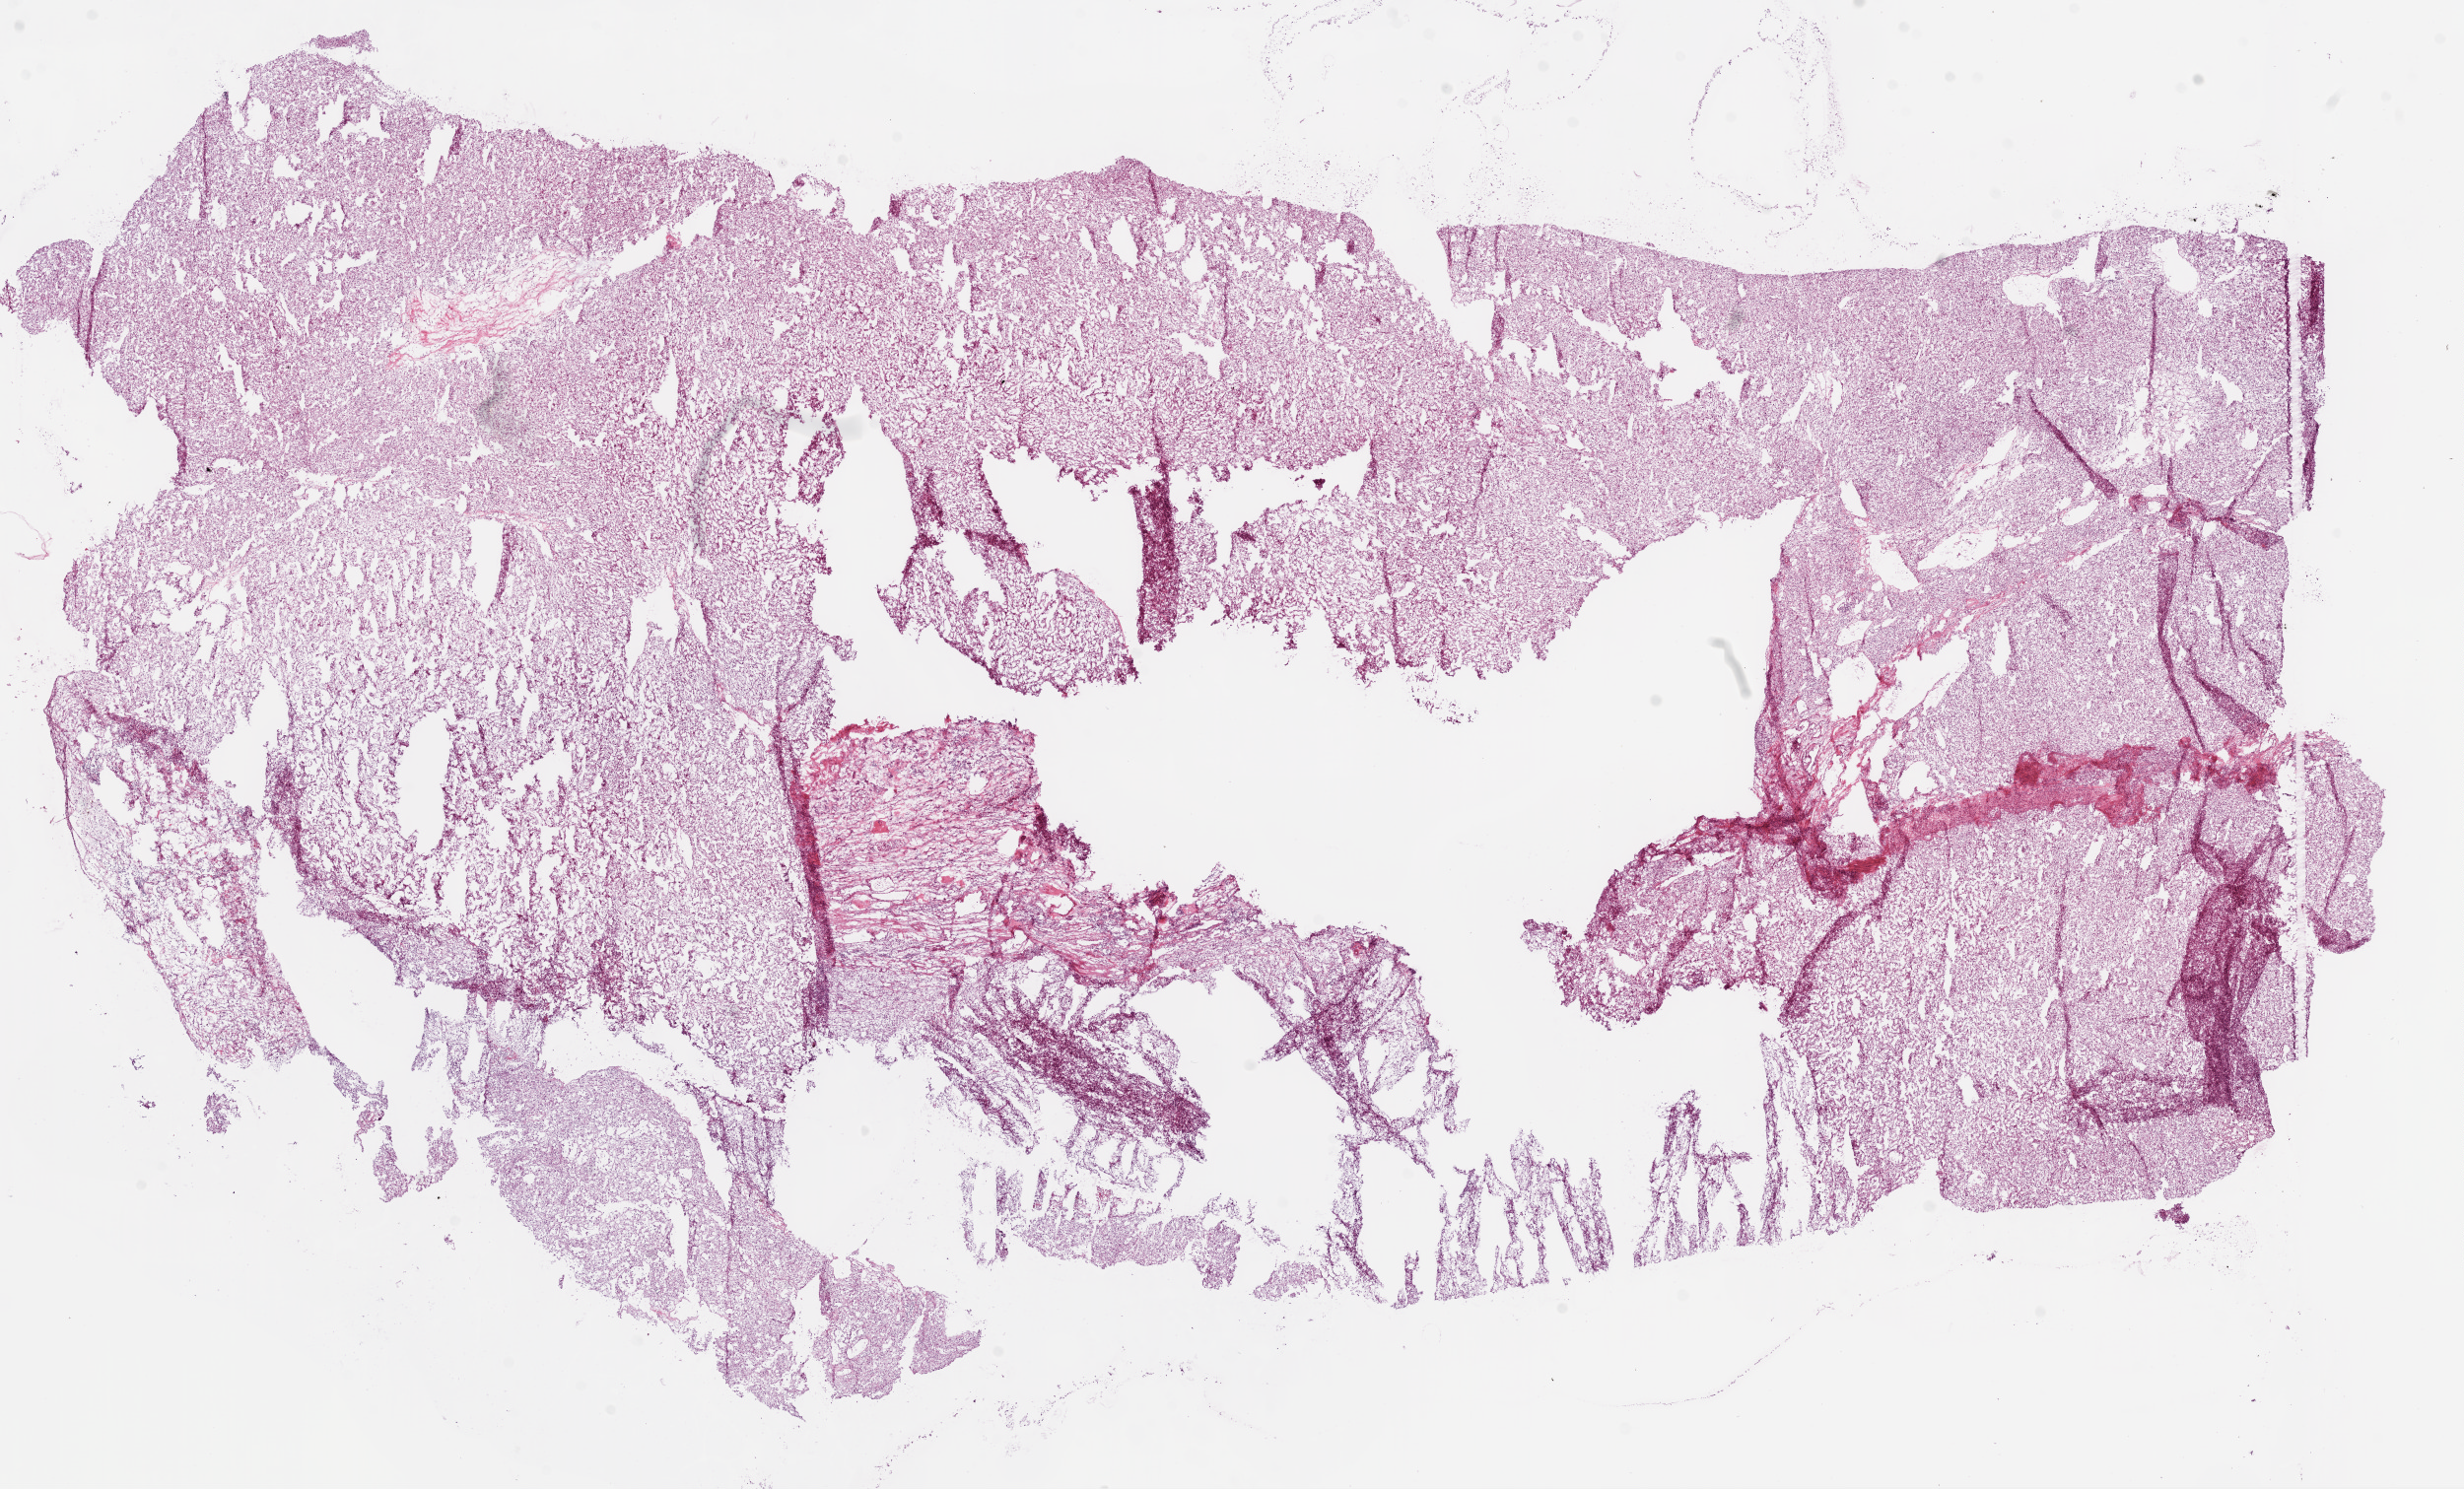
H&E-stained whole-slide image — shown as a low-resolution overview of the whole scanned area (about 20.1 x 12.1 mm, acquisition: 20x scan), frozen section from the bottom of the tissue portion, primary tumour sample from the kidney. Patient sex: female. Histologic grade: G2 (moderately differentiated). Composition of this section per pathologist review: tumour cells 90%, tumour nuclei 85%, normal cells 0%, stromal cells 10%, necrosis 0%.
- AJCC pathologic stage: I
- histologic diagnosis: Clear cell adenocarcinoma, NOS